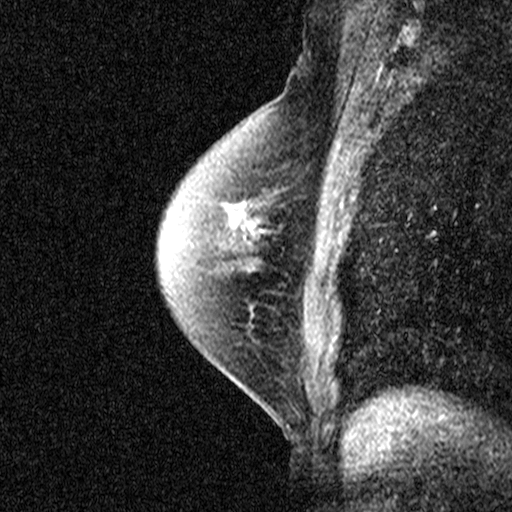
Breast MRI (dynamic contrast-enhanced), one sagittal slice; slice 27 of 40 in the series (ordered by position); dynamic contrast-enhanced study with each time point stored as its own series, time point 2 of 3 at this slice position (early post-contrast, ordered by acquisition time); 1.5 T; TE 4.5 ms, TR 11 ms; 3 mm slice thickness; 512 × 512 image matrix, field of view 200 × 200 mm. Female patient, age 55 years. Case-level facts recorded for this patient, not image findings: setting: breast cancer imaged before/during neoadjuvant chemotherapy; receptor status: HR-positive, HER2-negative.
Outlined on this slice (semi-automatically segmented with operator editing):
- analysis volume of interest (the breast-tissue region the enhancement analysis was run in; not a lesion): bounding box [x1, y1, x2, y2] px = [194, 202, 279, 277]
- tumour enhancement mask (voxels above the 90 % enhancement threshold inside the analysis volume of interest): [233, 212, 246, 238]